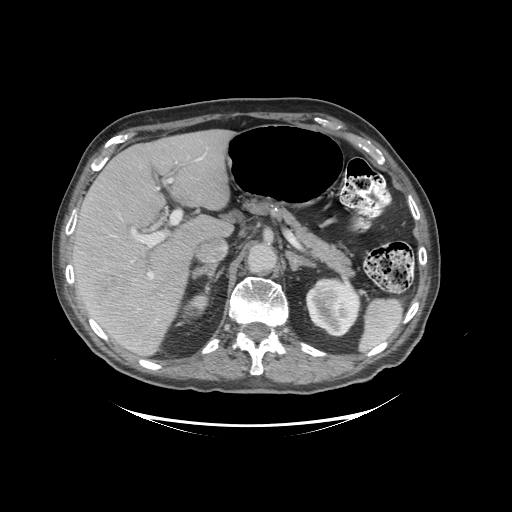
Contrast-enhanced abdominal CT (liver protocol), one axial slice; slice 63 of 99 in the series (ordered by position); reconstruction kernel STANDARD; soft-tissue window (W 400 / L 40 HU); 2.5 mm slice thickness; 512 × 512 image matrix. Case-level facts recorded for this patient, not image findings: diagnosis: hepatocellular carcinoma (patient treated with transarterial chemoembolisation; whether this scan precedes or follows treatment is not stated here); TNM stage (as recorded): Stage-I; Child-Pugh class: A; tumour nodularity: uninodular.
Structures marked on this image (semi-automatic segmentation, software-assisted and operator-edited):
- liver parenchyma outside the tumour (the mass and vessels are separate outlines, so this box may not span the whole liver): box from (x=72, y=130) to (x=232, y=354) px
- mass: (x=86, y=263)–(x=161, y=346)
- liver vessels: (x=132, y=157)–(x=203, y=279)